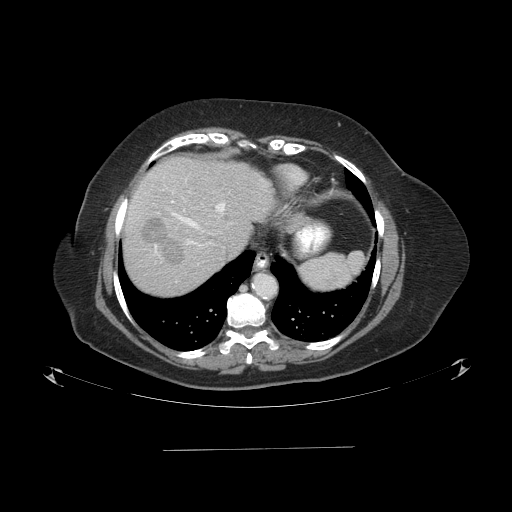
Contrast-enhanced abdominal CT (liver protocol), one axial slice; slice 75 of 103 in the series (ordered by position); 120 kVp; one of 2 acquisitions stored at this slice position; soft-tissue window (W 400 / L 40 HU); 2.5 mm slice thickness; 512 × 512 image matrix, field of view 500 × 500 mm. From the clinical record (not read from this slice): diagnosis: hepatocellular carcinoma (patient treated with transarterial chemoembolisation; whether this scan precedes or follows treatment is not stated here); TNM stage (as recorded): Stage-IIIA.
Structures marked on this image (semi-automatic segmentation, software-assisted and operator-edited):
- liver parenchyma outside the tumour (the mass and vessels are separate outlines, so this box may not span the whole liver): bounding box <124,156,274,294> (left, top, right, bottom; pixels)
- mass: <142,217,184,265>
- liver vessels: <136,191,225,245>